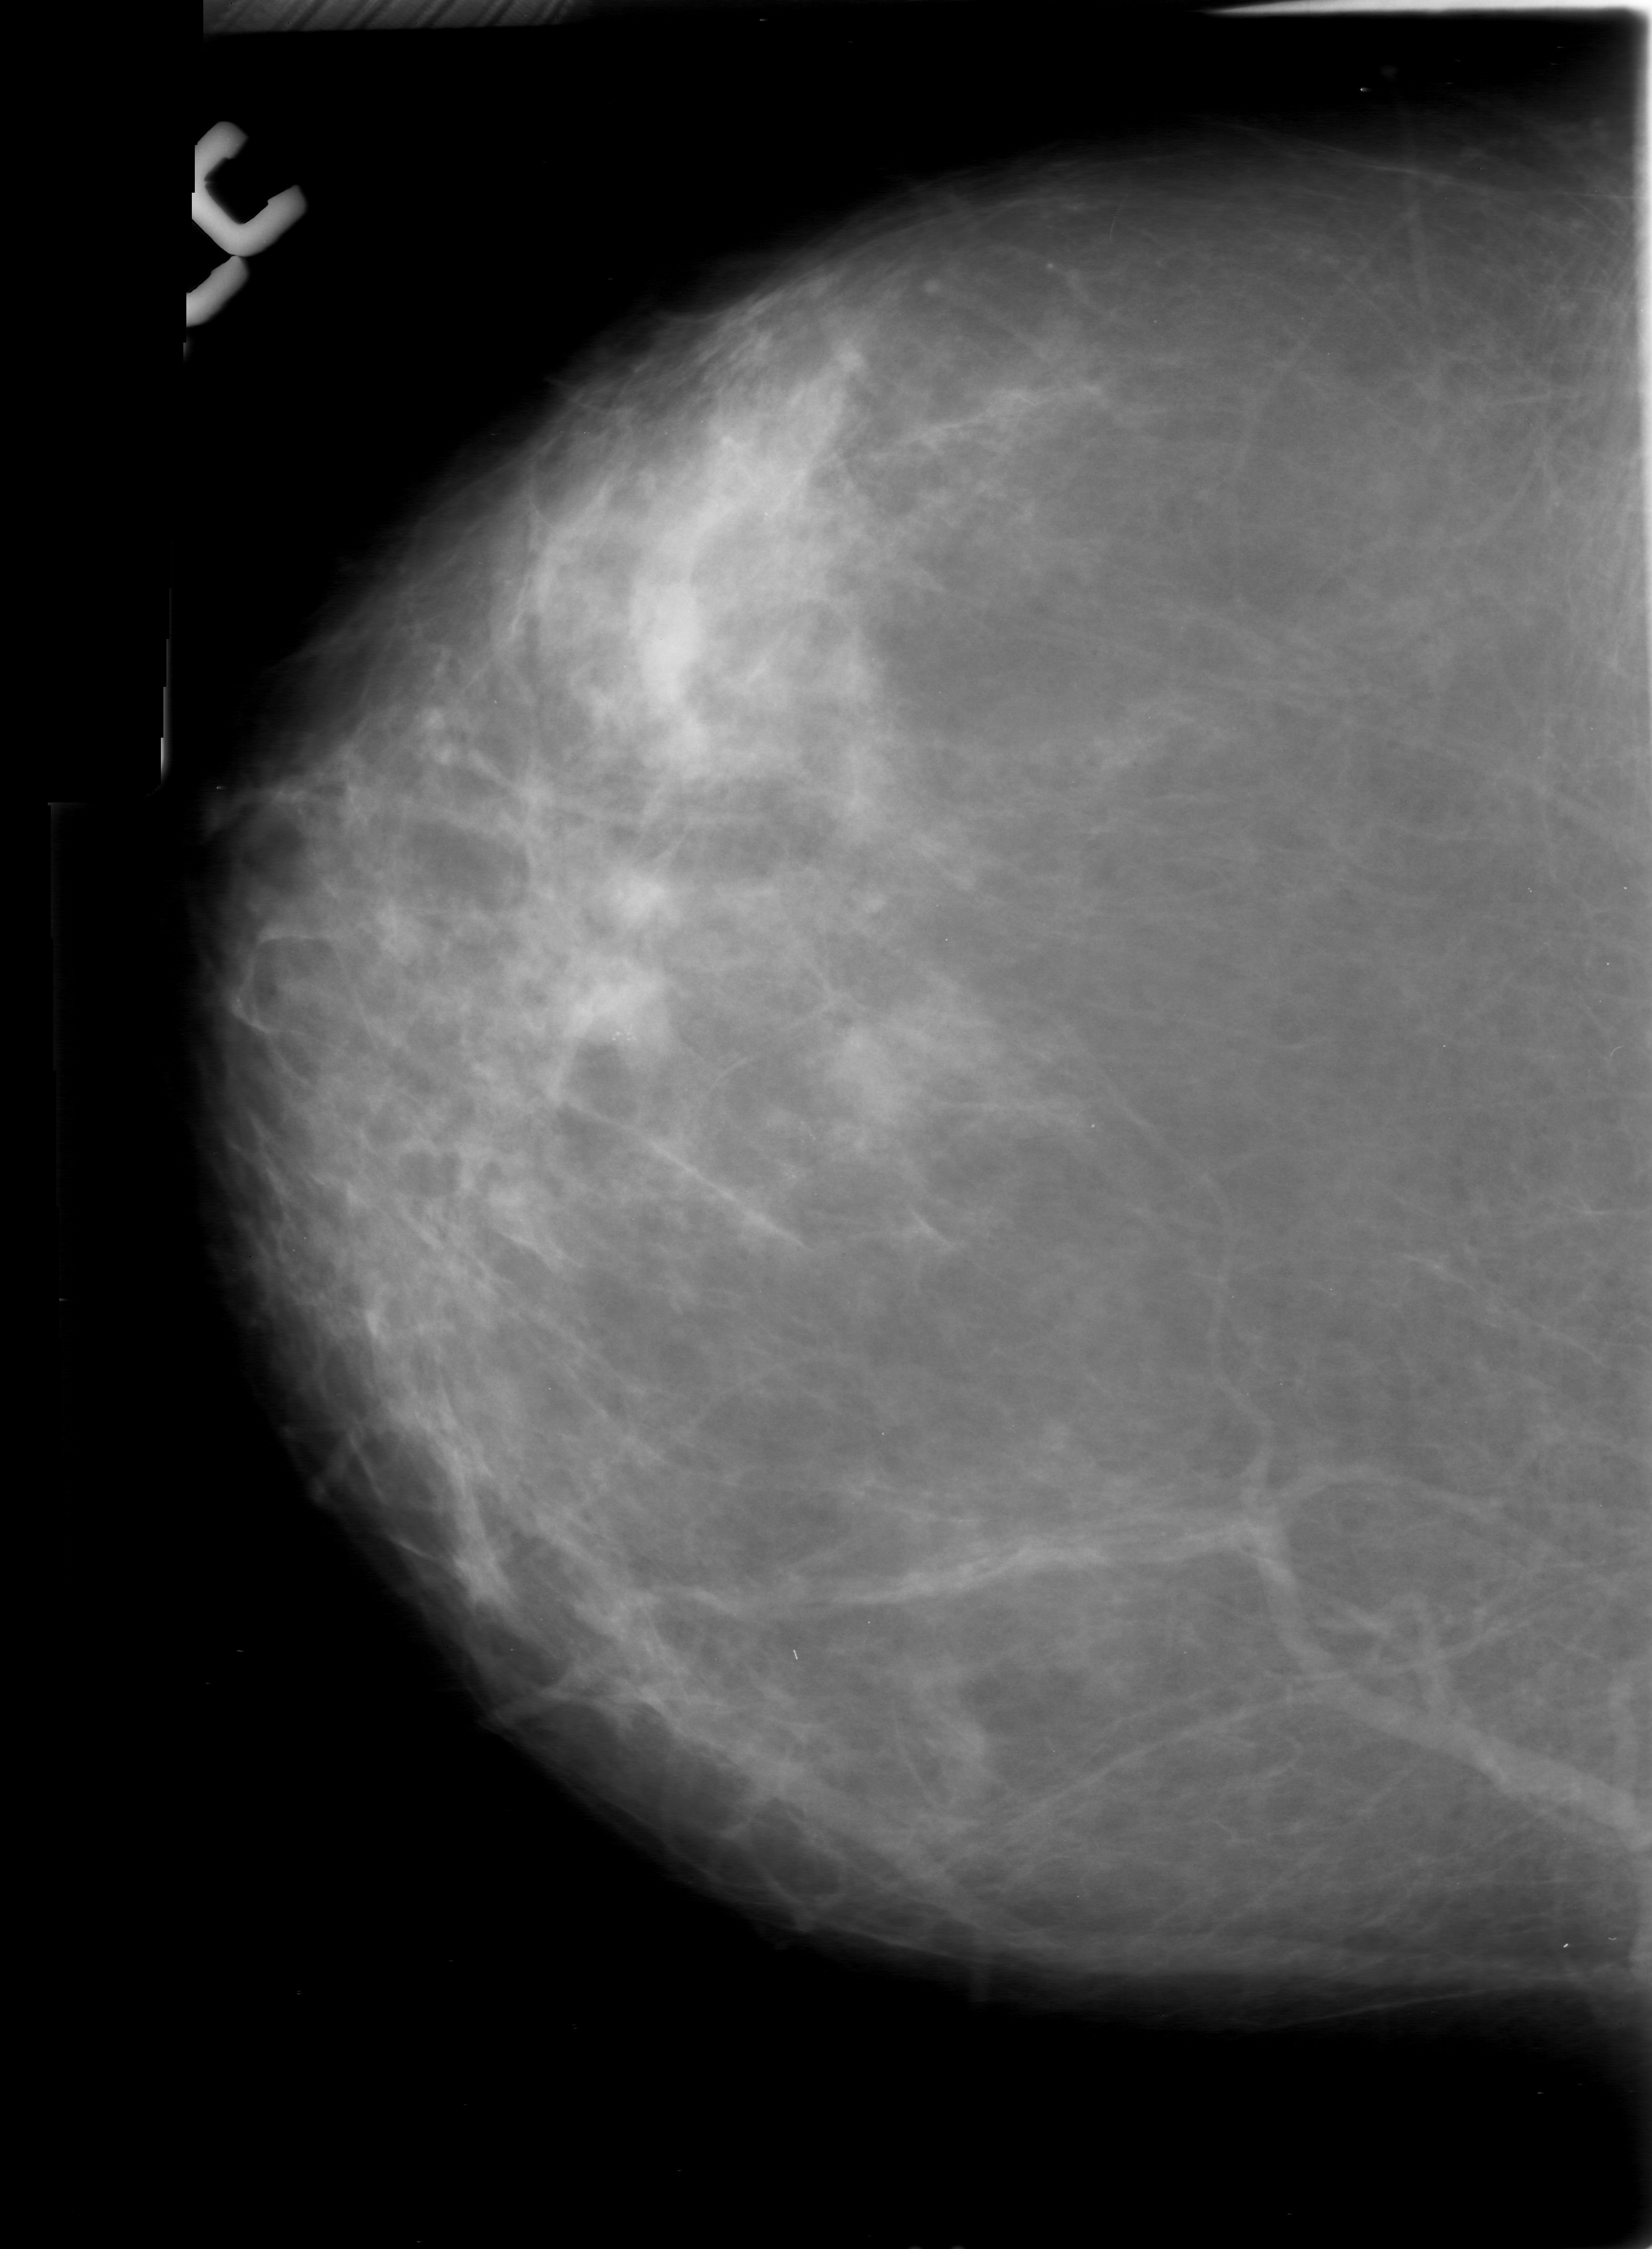
Scanned film-screen mammogram; right breast; CC view; BI-RADS breast density category 2 (scale 1–4).
- Radiologist-marked abnormalities on this image: calcifications, morphology pleomorphic, distribution clustered; BI-RADS assessment category 0 (incomplete: needs additional imaging); pathology result (as recorded, not read from the image): malignant.